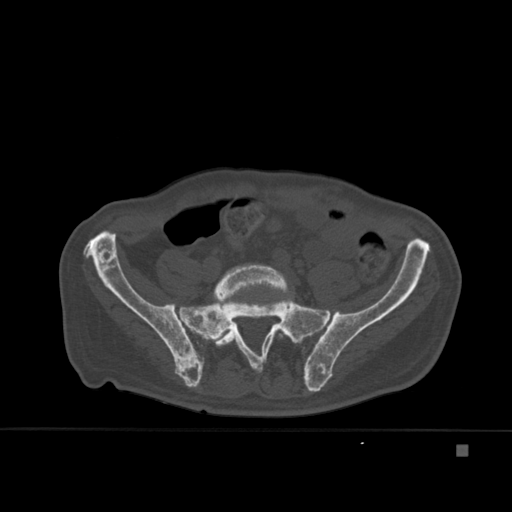
CT including the spine, one axial slice. Slice 93 of 451 in the series (ordered by position). Bone window (W 1800 / L 400 HU). 1.5 mm slice thickness. 512 × 512 image matrix. Patient: male, 75 years. Case-level facts recorded for this patient, not image findings: primary cancer: prostate.
Structures marked on this image (semi-automatically segmented with operator editing):
- L5 vertebra: box from (x=213, y=264) to (x=287, y=355) px